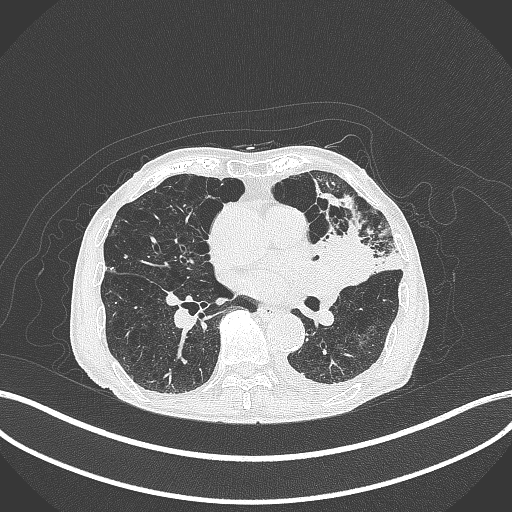
Chest CT, one axial slice; slice 181 of 385 in the series (ordered by position); lung window (W 1500 / L -600 HU); 1 mm slice thickness; 512 × 512 image matrix, field of view 400 × 400 mm. Patient: male, 90 years or older. Case-level facts recorded for this patient, not image findings: clinical TNM (as recorded): T2b N1 M0.
Outlined on this slice (rectangle marked by the reading radiologist):
- lung tumour (recorded histology: squamous cell carcinoma): box from (x=317, y=227) to (x=375, y=289) px